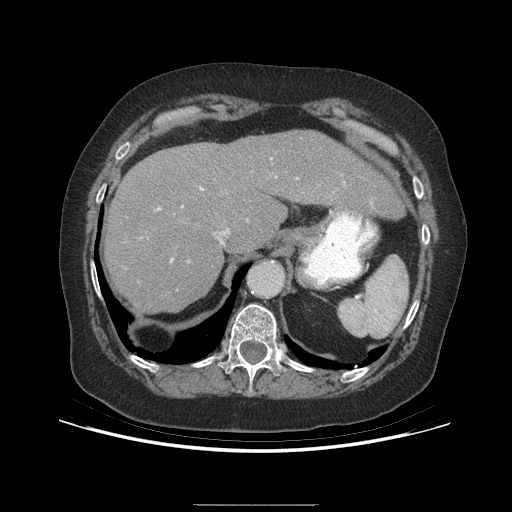
Contrast-enhanced abdominal CT (liver protocol), one axial slice. Position 169 of 192 along the scan axis. Reconstruction kernel STANDARD. 140 kVp. Soft-tissue window (W 400 / L 40 HU). 512 × 512 image matrix. From the clinical record (not read from this slice): diagnosis: hepatocellular carcinoma (patient treated with transarterial chemoembolisation; whether this scan precedes or follows treatment is not stated here); TNM stage (as recorded): Stage-I; Child-Pugh class: A; tumour size: 3.2 cm.
Structures marked on this image (semi-automatic segmentation, software-assisted and operator-edited):
- liver parenchyma outside the tumour (the mass and vessels are separate outlines, so this box may not span the whole liver): bounding box <104,130,404,312> (left, top, right, bottom; pixels)
- liver vessels: <157,158,272,262>